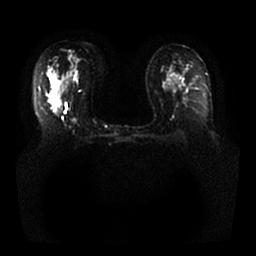
Breast MRI, one axial slice. Slice 16 of 25 in the series (ordered by position). Diffusion-weighted series; image 2 of 4 stored at this slice position (different b-values; order by instance number). 1.5 T. 256 × 256 image matrix. Female patient.
Structures marked on this image (outlined manually by an expert reader):
- tumour on diffusion-weighted imaging: bounding box (x1, y1, x2, y2) in pixels: (58, 107, 63, 113)